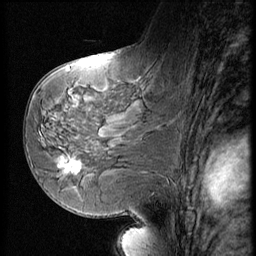
Breast MRI (dynamic contrast-enhanced), one sagittal slice. Slice 27 of 56 in the series (ordered by position). Dynamic contrast-enhanced series, image 2 of 3 at this slice position (ordered by acquisition). 1.5 T. TE 4.2 ms, TR 9 ms. 256 × 256 image matrix, field of view 180 × 180 mm. Female patient, age 58 years. Case-level facts recorded for this patient, not image findings: setting: breast cancer imaged before/during neoadjuvant chemotherapy; receptor status: HR-positive, HER2-negative.
Structures marked on this image (semi-automatic segmentation, software-assisted and operator-edited):
- analysis volume of interest (the breast-tissue region the enhancement analysis was run in; not a lesion): box from (x=51, y=147) to (x=96, y=185) px
- tumour enhancement mask (voxels above the 140 % enhancement threshold inside the analysis volume of interest): (x=59, y=157)–(x=82, y=176)